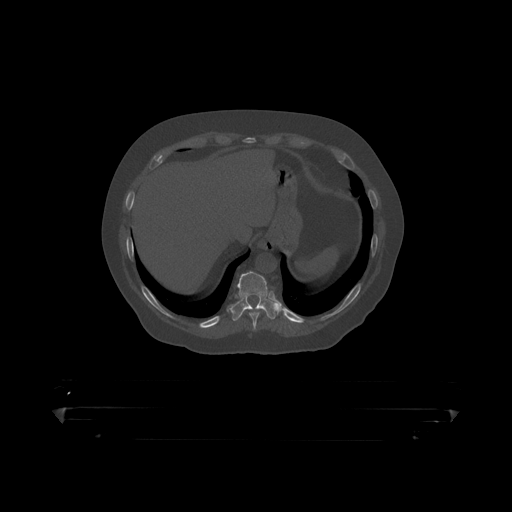
CT including the spine, one axial slice; slice 222 of 390 in the series (ordered by position); reconstruction kernel STANDARD; bone window (W 1800 / L 400 HU); 512 × 512 image matrix, field of view 650 × 650 mm. Patient: male, 60 years. Case-level facts recorded for this patient, not image findings: primary cancer: prostate.
Outlined on this slice (semi-automatic segmentation, software-assisted and operator-edited):
- T10 vertebra: bounding box <231,272,279,318> (left, top, right, bottom; pixels)
- T9 vertebra: <249,308,260,319>